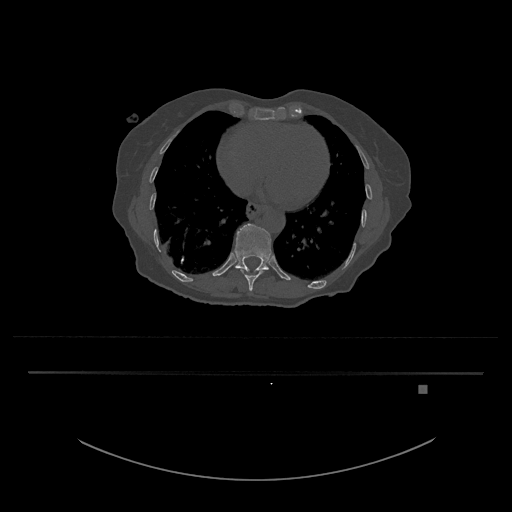
CT including the spine, one axial slice. Position 687 of 797 along the scan axis. Reconstruction kernel Br40s/3. Bone window (W 1800 / L 400 HU). 0.5 mm slice thickness. 512 × 512 image matrix, field of view 500 × 500 mm. Patient: female, 57 years. From the clinical record (not read from this slice): primary cancer: cervical.
Outlined on this slice (semi-automatically segmented with operator editing):
- T10 vertebra: bounding box [x1, y1, x2, y2] px = [239, 269, 267, 291]
- T11 vertebra: [234, 224, 271, 271]